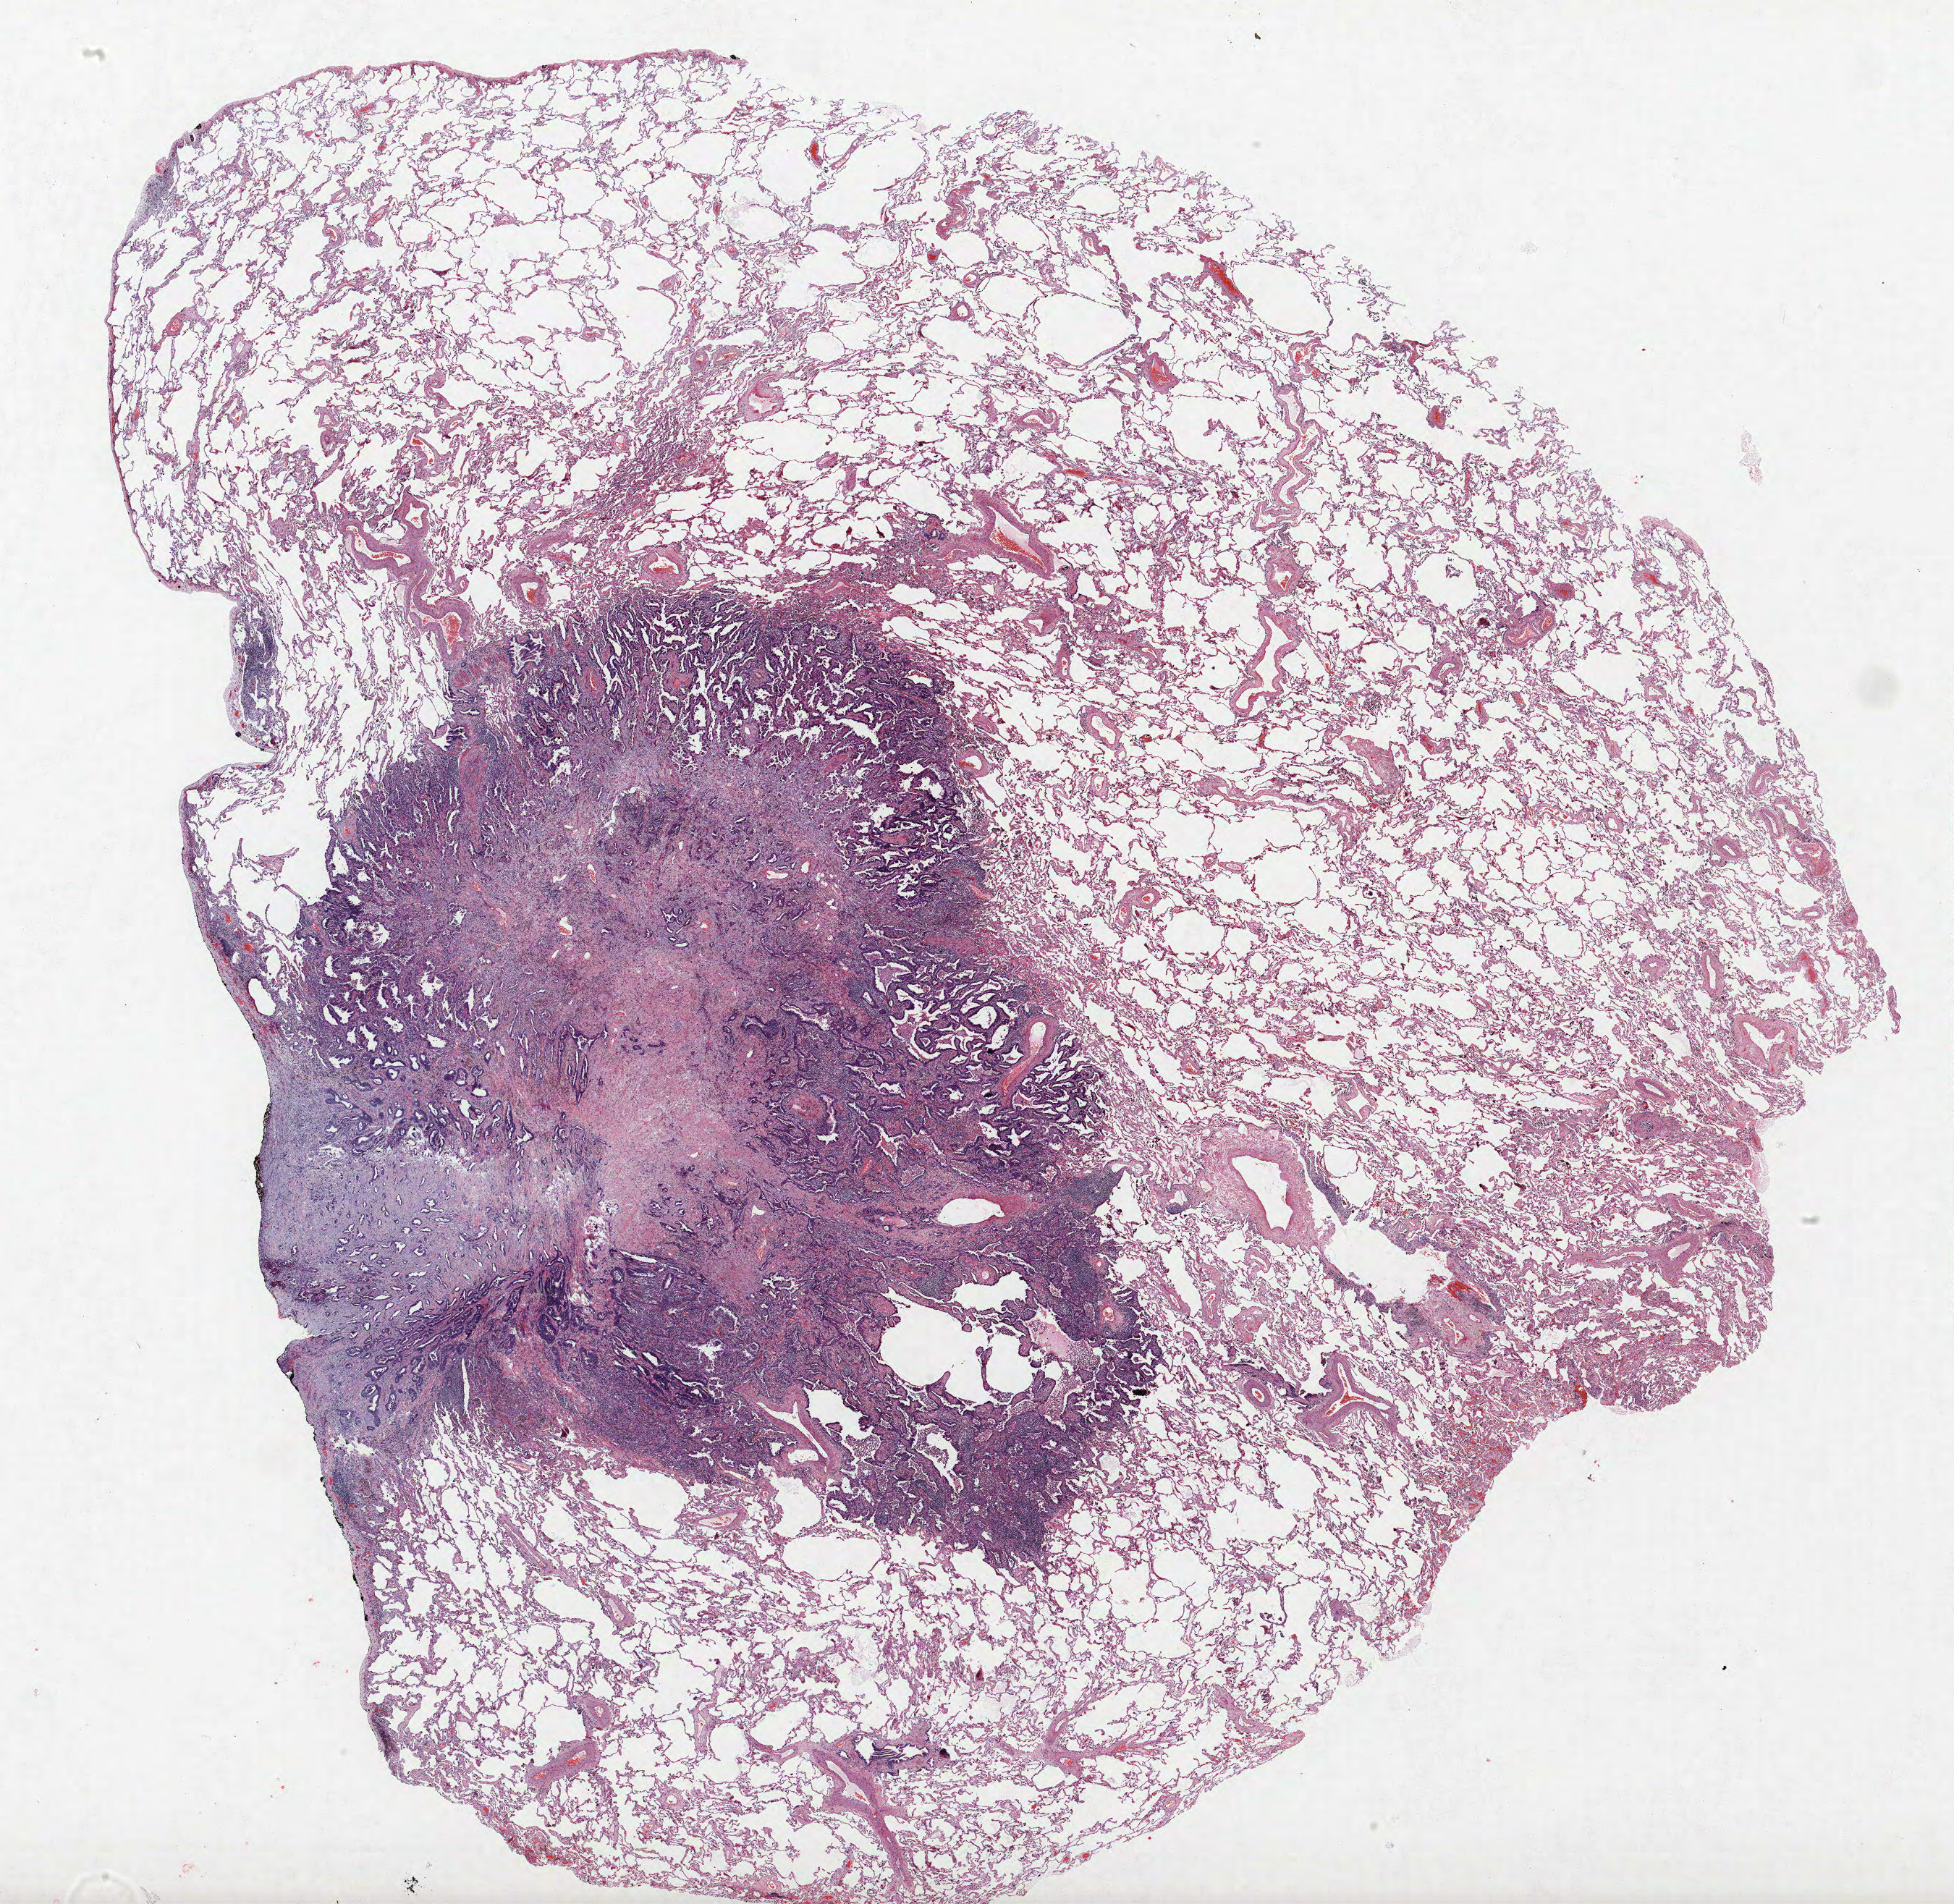
H&E-stained whole-slide image, a low-resolution overview of the entire scanned area, about 21.6 x 21.1 mm (slide scanned at 40x), FFPE section, lung tissue. Female, age 58 at enrolment. Former smoker at enrolment. Grade: well differentiated (G1).
Tumour size (pathology): 10 mm. Primary tumour location (clinical record): right lower lobe. Stage (AJCC 6th edition): IB. Participant's lung-cancer diagnosis: Adenocarcinoma, NOS.